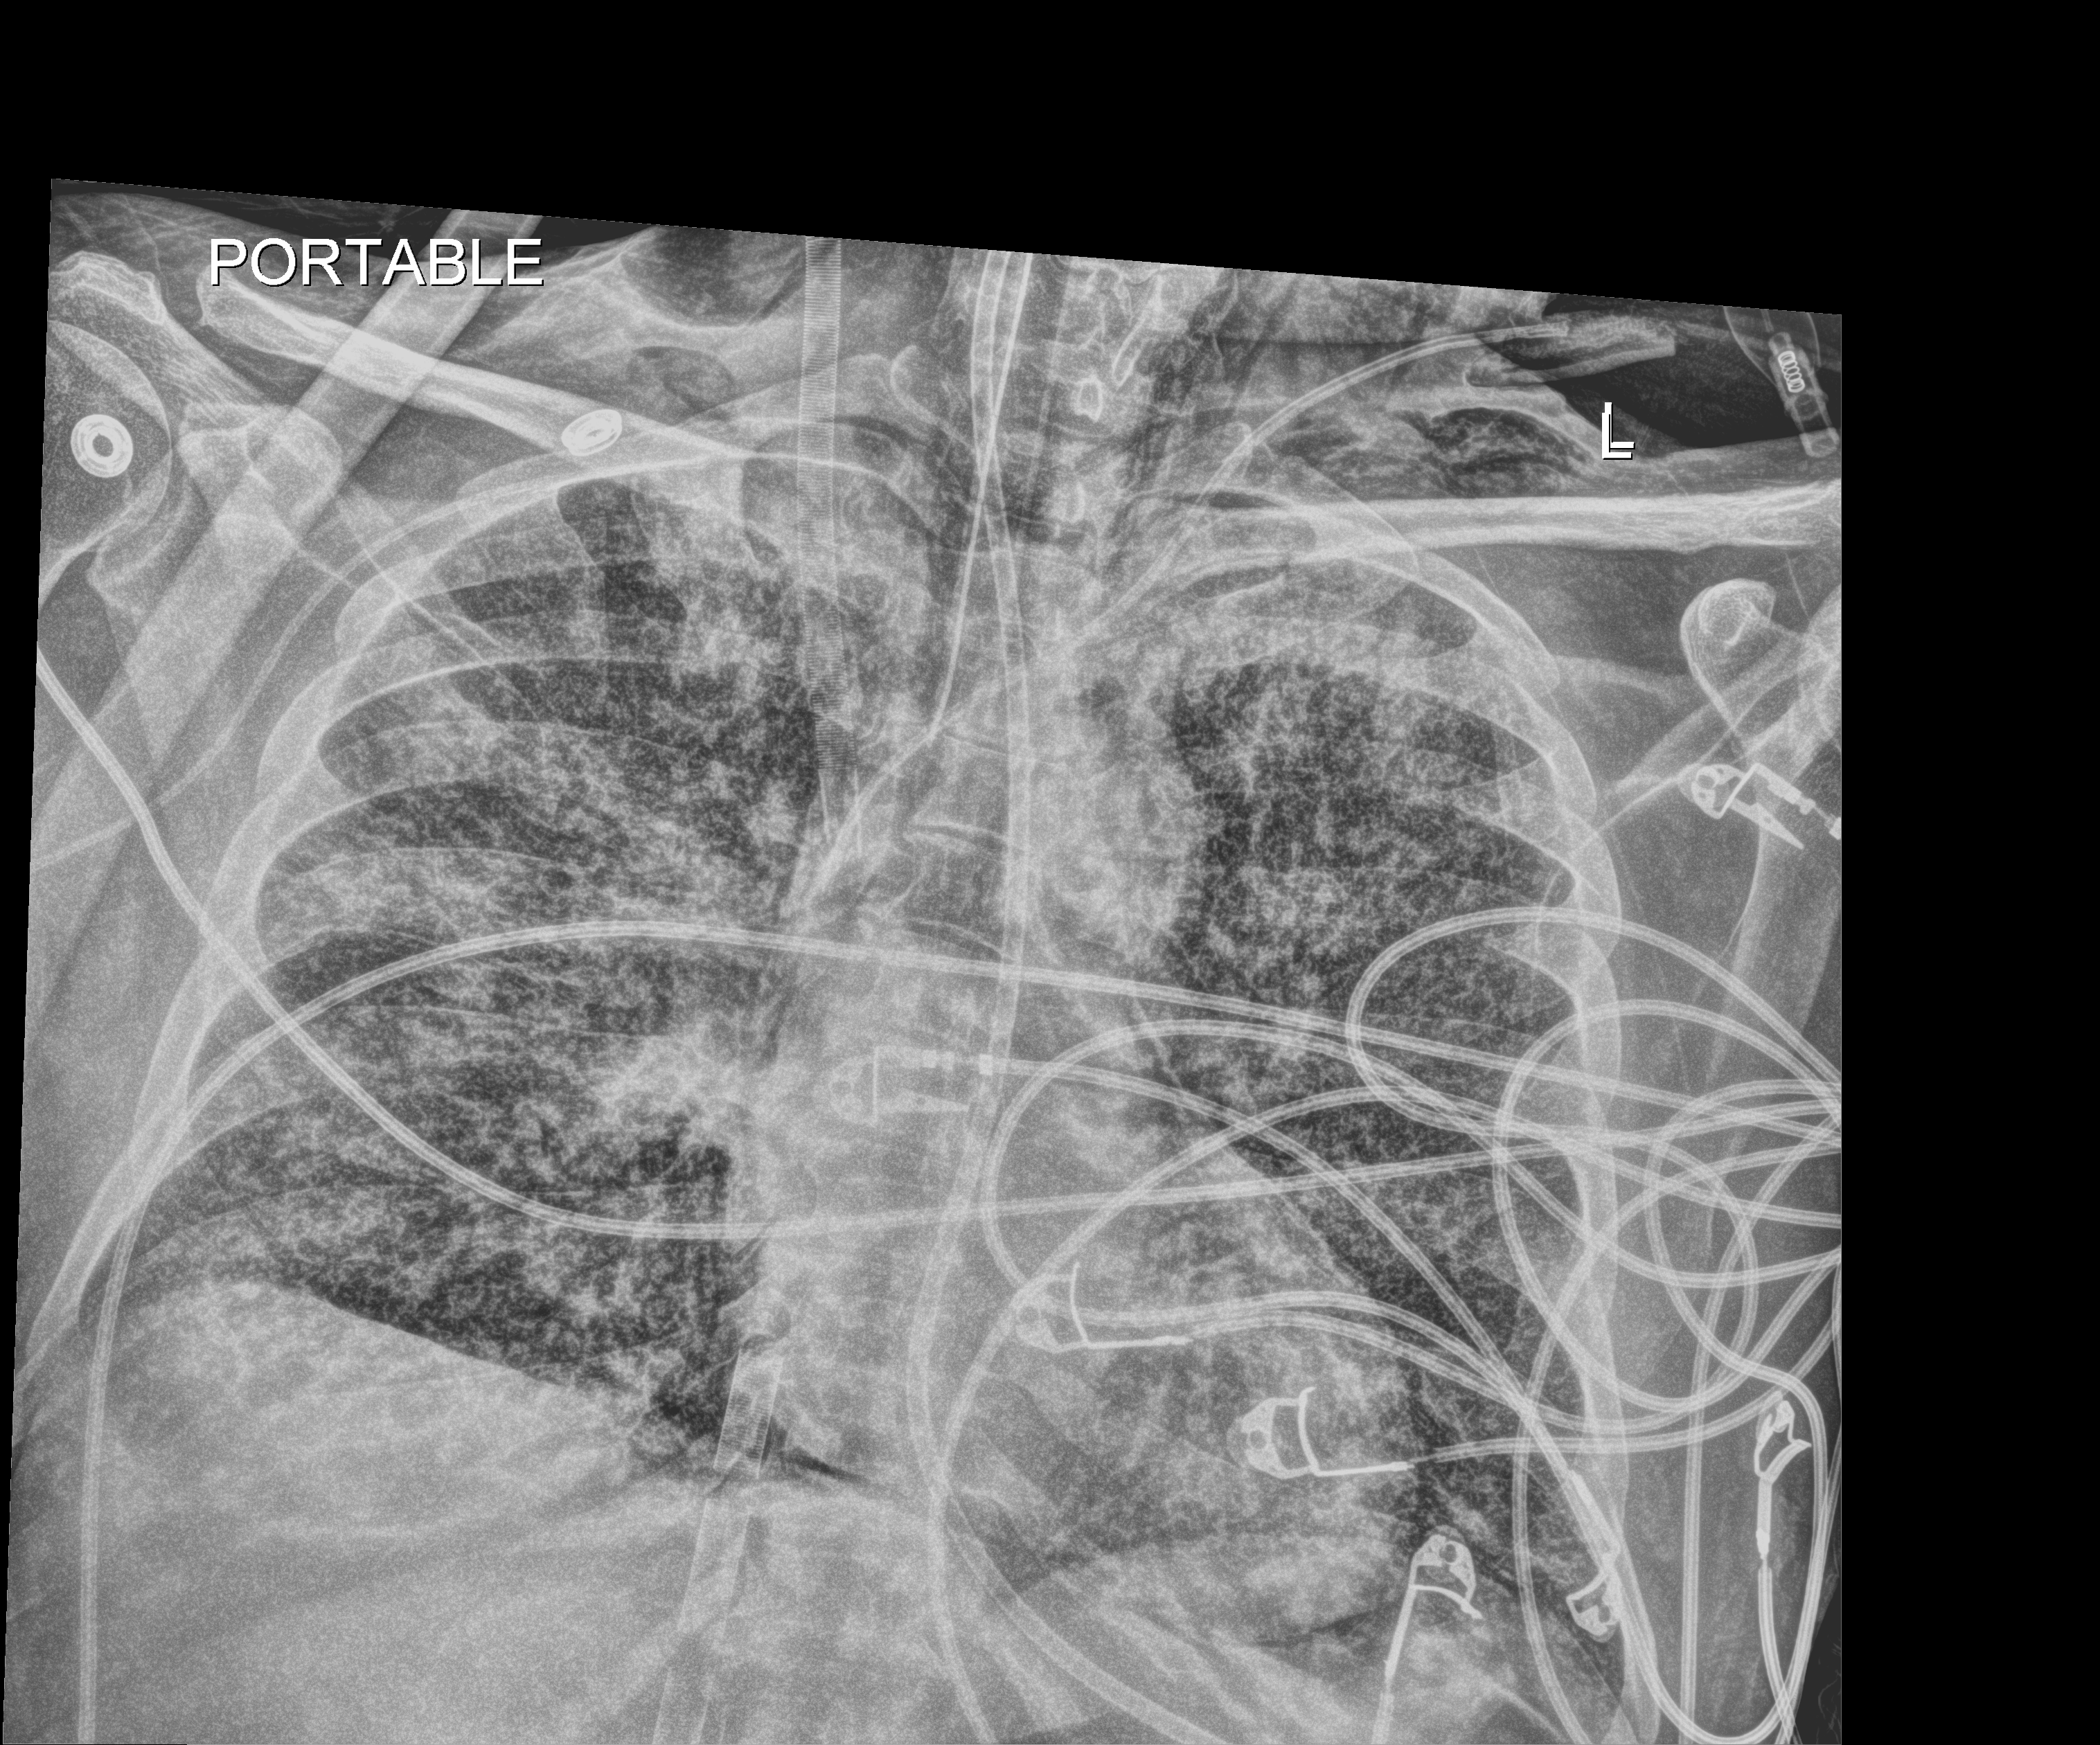
Chest X-ray. Male patient hospitalised with COVID-19, age 18–59 years.
Admission-level facts for this patient (not findings on this image; timing relative to this image not recorded): chronic kidney disease (admission record): no; admitted to intensive care during this hospital stay: yes; mechanically ventilated during this hospital stay: yes.